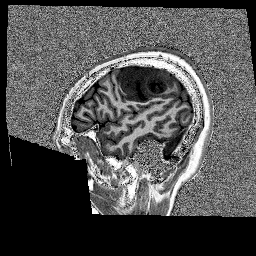
Brain MRI from a brain-tumour surgery series, one sagittal slice. Slice 39 of 176 in the series (ordered by position). 256 × 256 image matrix, field of view 256 × 256 mm. Case-level facts recorded for this patient, not image findings: histopathology: Glioblastoma; WHO grade: 4; IDH mutation: no; tumour location: Left Frontal.
Structures marked on this image (outlined manually by an expert reader):
- tumour: bounding box [x1, y1, x2, y2] px = [118, 64, 175, 101]